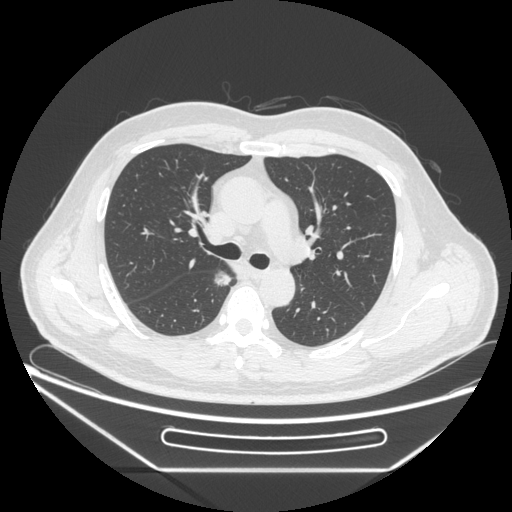
Chest CT, one axial slice. Position 163 of 271 along the scan axis. Reconstruction kernel STANDARD. 120 kVp. Lung window (W 1500 / L -600 HU). 1.25 mm slice thickness. 512 × 512 image matrix, field of view 414 × 414 mm. Male patient, age 49 years. Case-level facts recorded for this patient, not image findings: clinical TNM (as recorded): T1b N0 M0; histopathological grade: G2.
Structures marked on this image (rectangle marked by the reading radiologist):
- lung tumour (recorded histology: adenocarcinoma): bounding box <209,262,234,289> (left, top, right, bottom; pixels)